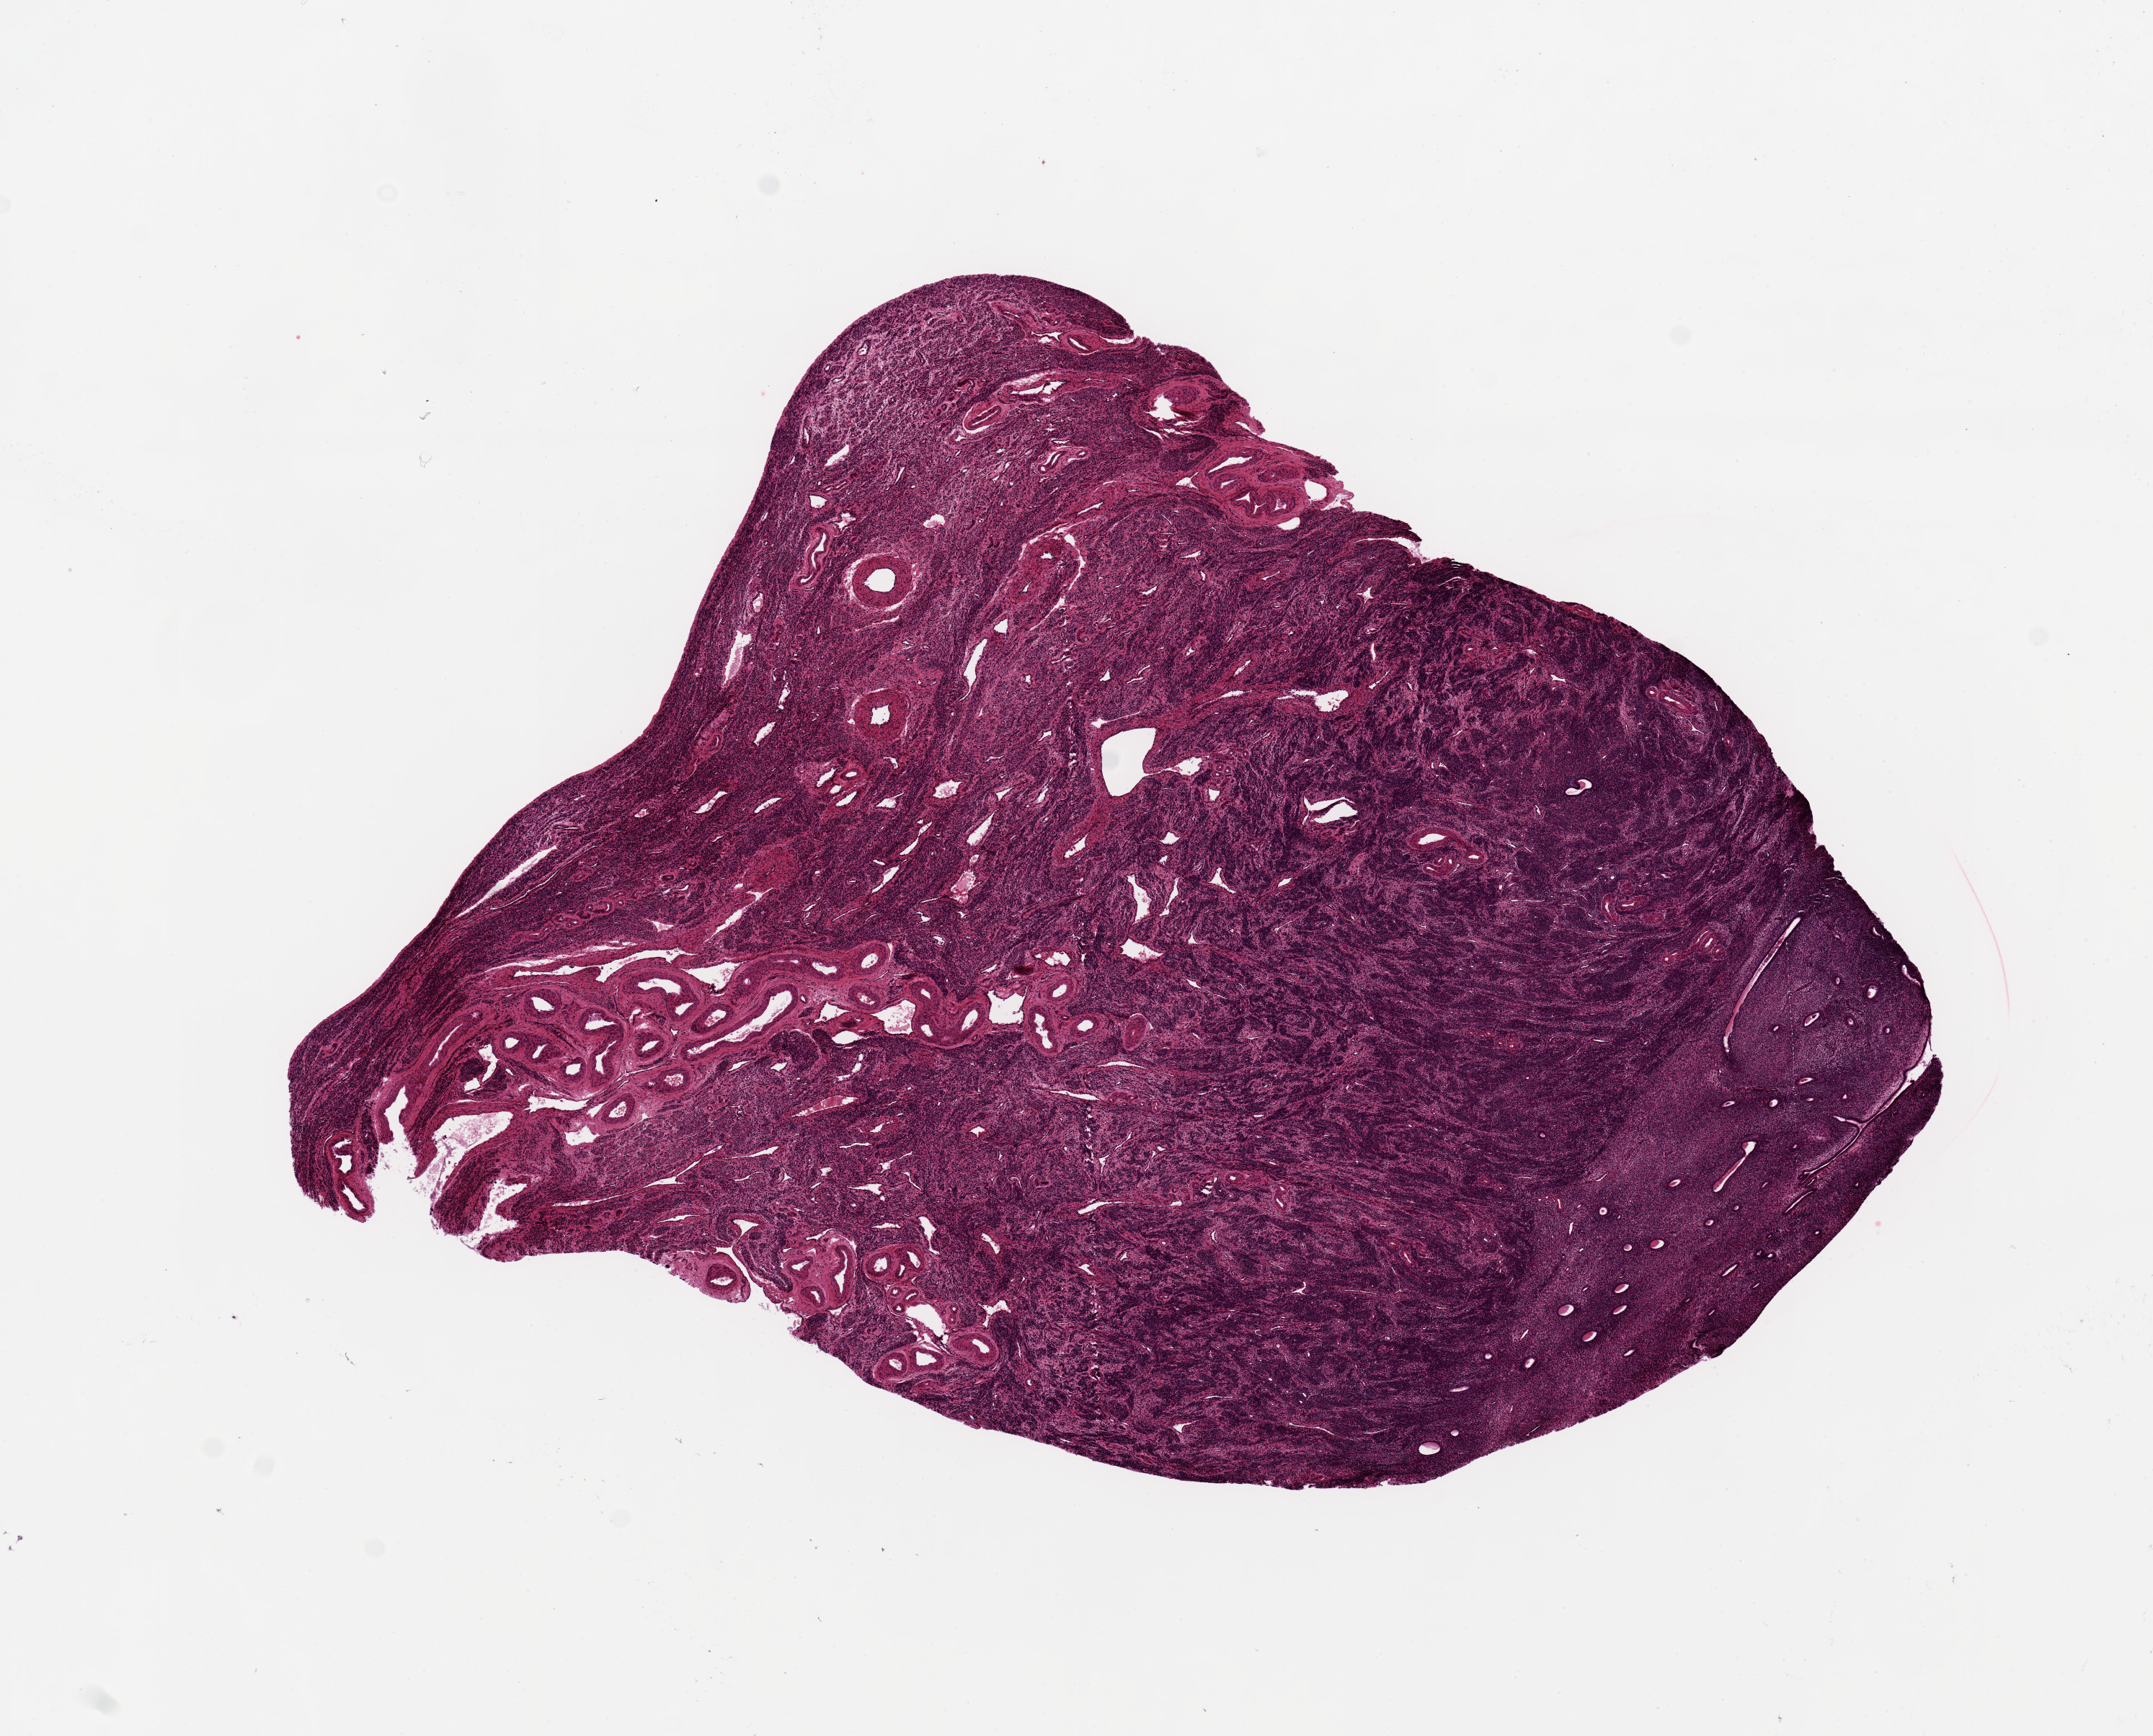
Whole-slide image, H&E stain, whole scanned area (about 11.8 x 9.5 mm, from a 20x scan) shown as a low-resolution overview; PAXgene-fixed paraffin-embedded (PFPE) section; sampled site (target tissue): uterus; tissue donor sample. Donor sex: female.
Review note (as recorded): ~7x6mm piece; a 3.3x1.2mm area of weakly proliferative stroma/glands on one edge.